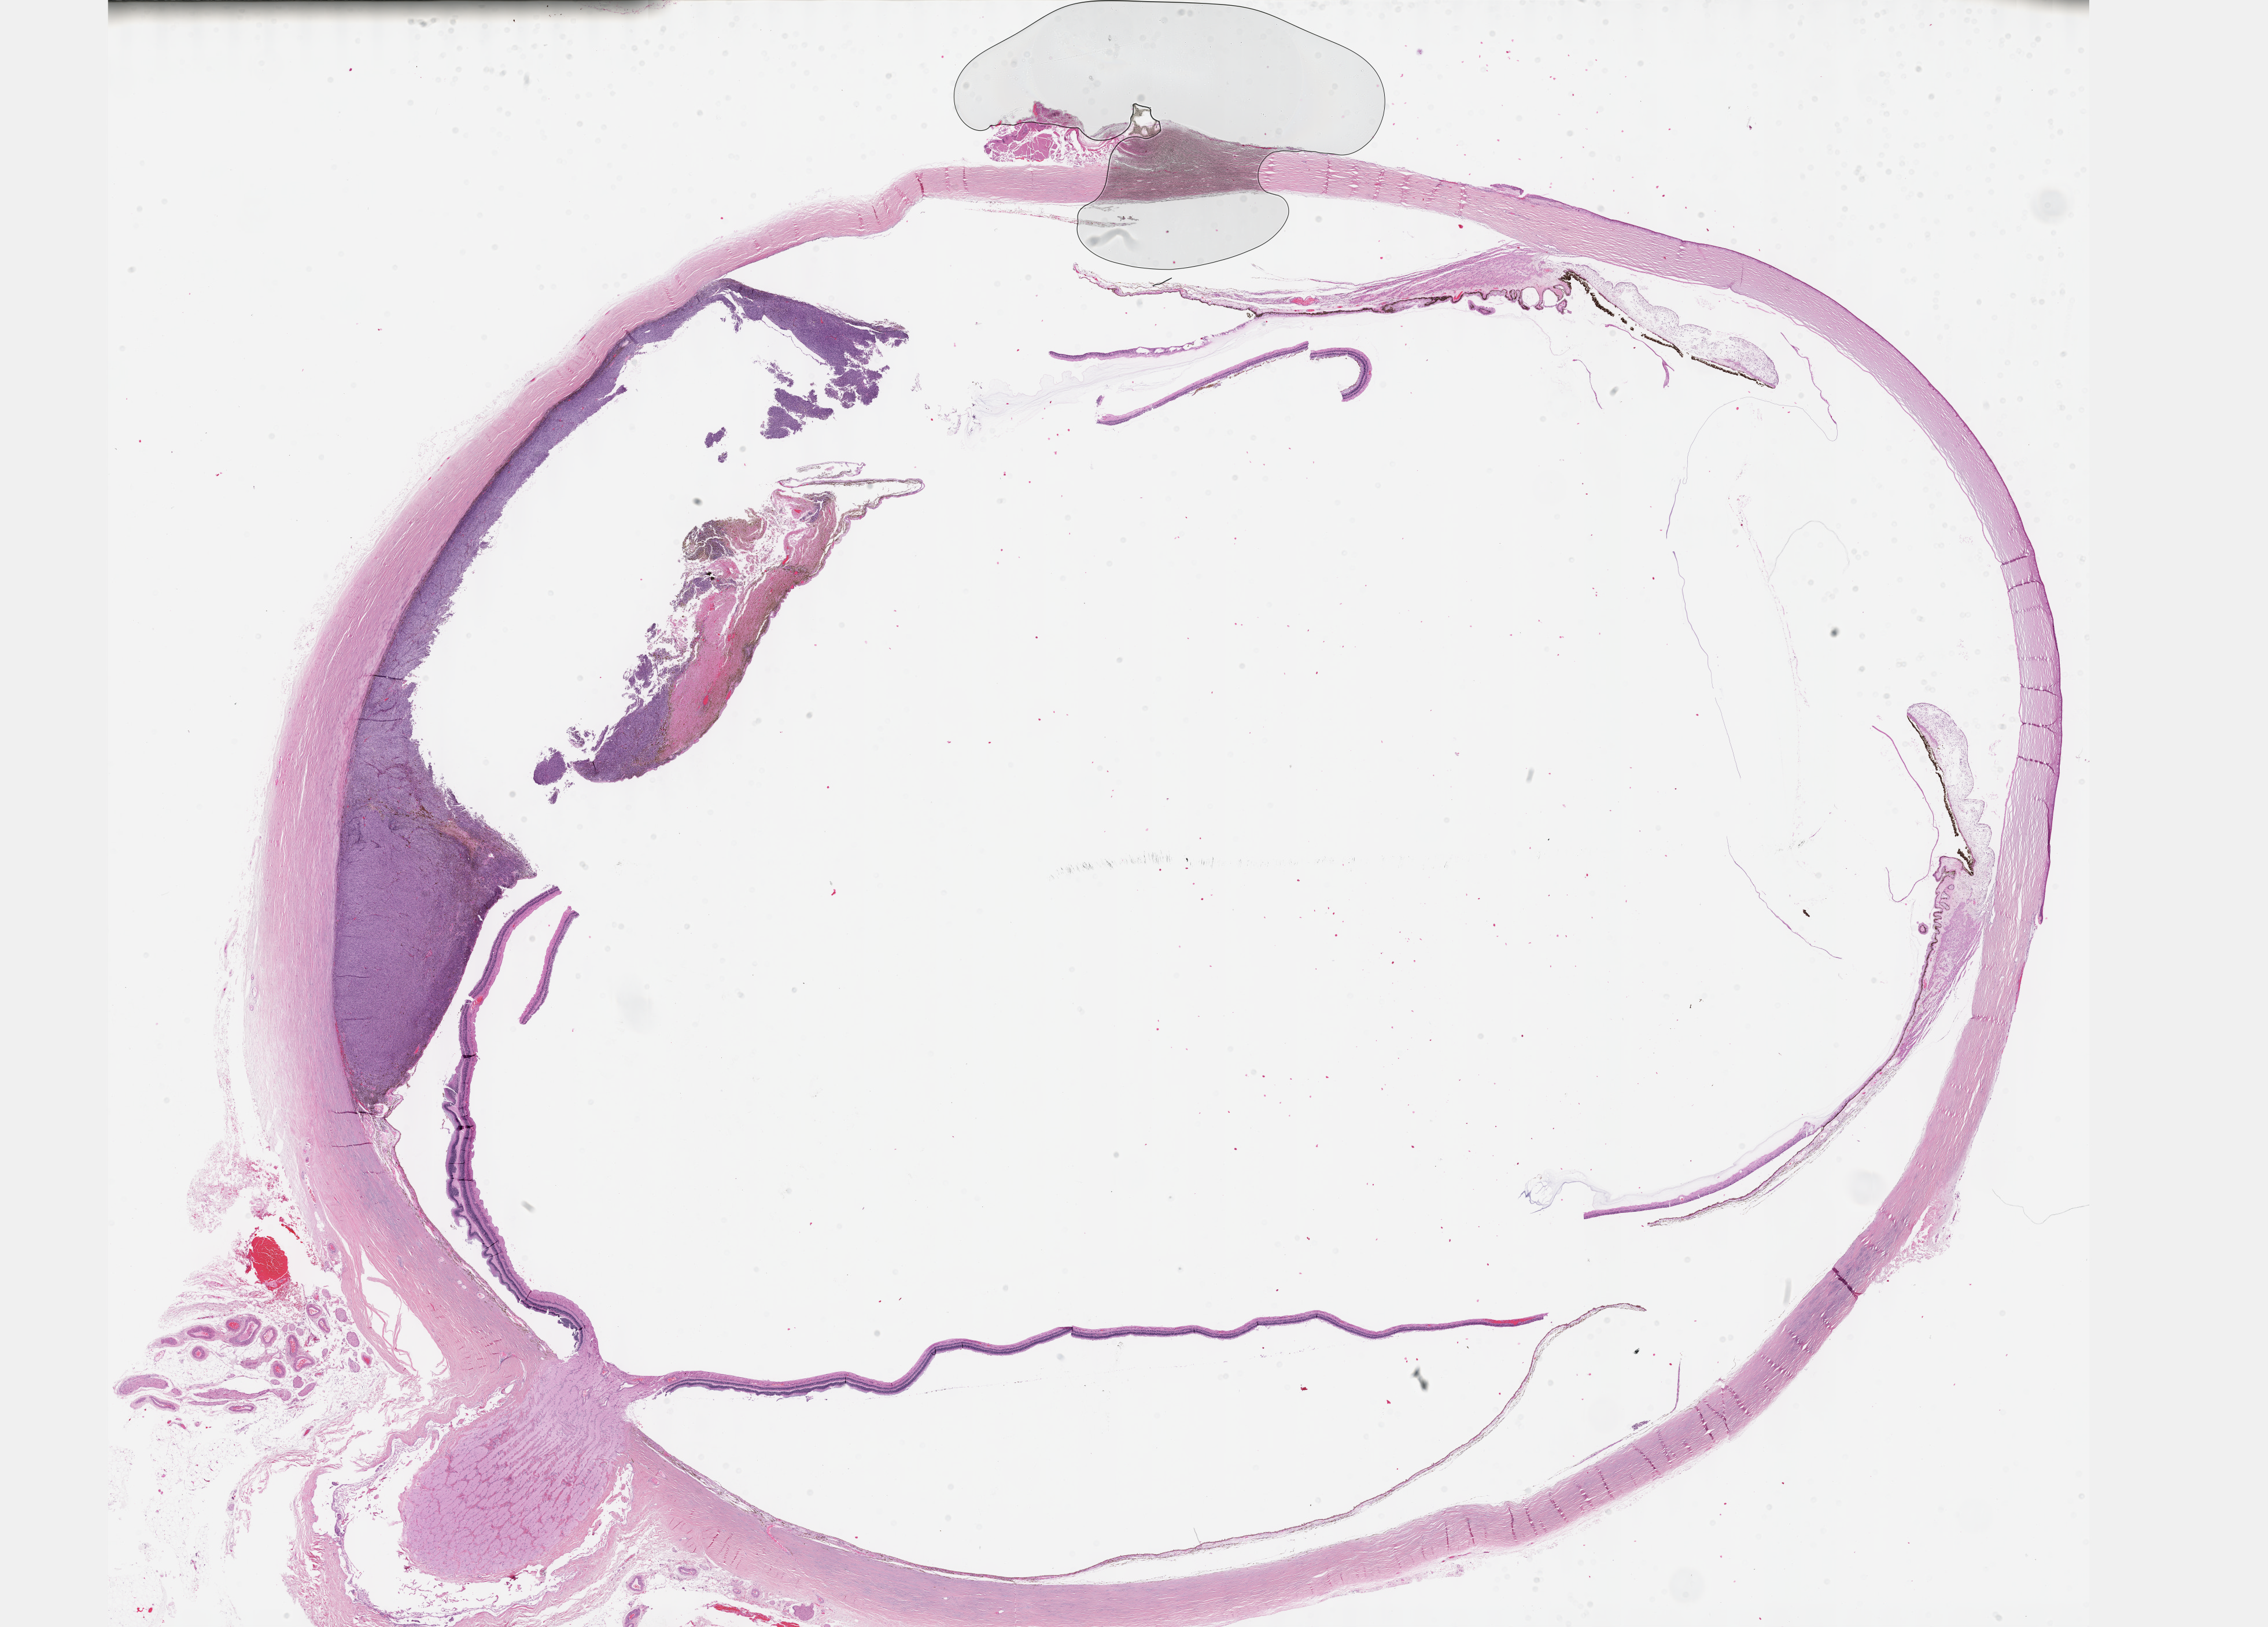
H&E whole-slide image — a low-resolution overview of the entire scanned area, about 31.7 x 22.7 mm (from a 40x scan); formalin-fixed paraffin-embedded (FFPE) diagnostic section; primary tumour sample from the uvea. Female, age 70 years at initial diagnosis.
* AJCC pathologic stage: IIA (7th edition)
* diagnosis: Spindle cell melanoma, NOS (choroid)
* laterality: right